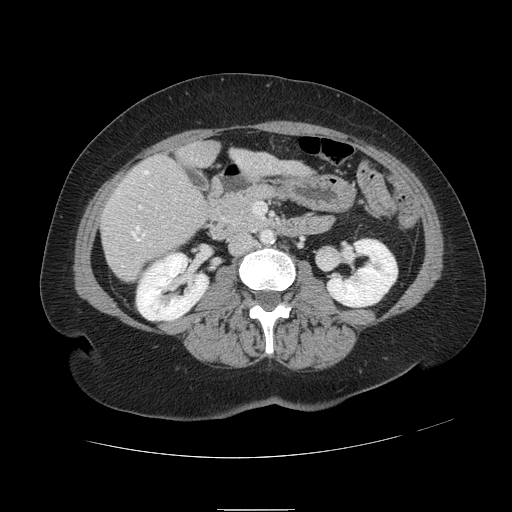
Contrast-enhanced abdominal CT, one axial slice; position 30 of 121 along the scan axis; 120 kVp; intravenous contrast given; soft-tissue window (W 400 / L 40 HU); 512 × 512 image matrix, field of view 400 × 400 mm. Female patient, age 52 years. From the clinical record (not read from this slice): diagnosis: colorectal cancer liver metastases, imaged before liver resection; multiple liver metastases: yes; largest metastasis: 6.3 cm; chemotherapy before resection: yes.
Outlined on this slice (manually delineated by an expert):
- hepatic veins: bounding box (x1, y1, x2, y2) in pixels: (122, 172, 150, 267)
- liver: (101, 143, 299, 281)
- planned liver remnant (the part of the liver to remain after resection): (180, 143, 299, 174)
- portal vein (with intrahepatic branches): (139, 206, 142, 210)